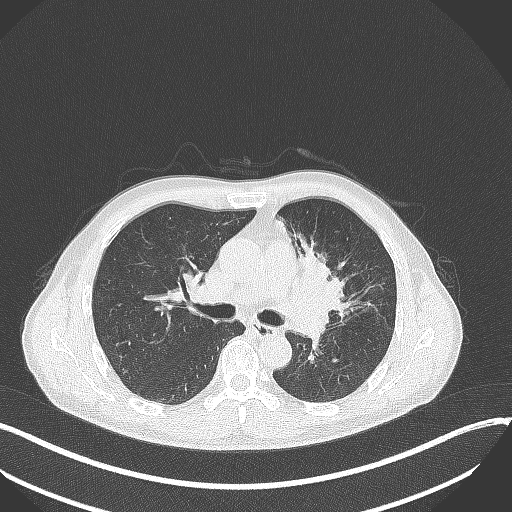
Chest CT, one axial slice; position 204 of 411 along the scan axis; reconstruction kernel B70f; lung window (W 1500 / L -600 HU); 1 mm slice thickness; 512 × 512 image matrix, field of view 400 × 400 mm. Patient: male, 56 years. From the clinical record (not read from this slice): clinical TNM (as recorded): T2a N0 M0.
Outlined on this slice (bounding box drawn by a radiologist):
- lung tumour (recorded histology: squamous cell carcinoma): bounding box (x1, y1, x2, y2) in pixels: (290, 240, 355, 323)